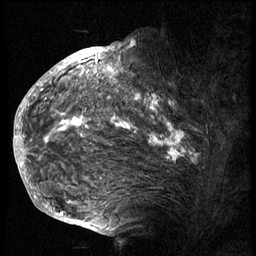
Breast MRI (dynamic contrast-enhanced), one sagittal slice. Slice 48 of 74 in the series (ordered by position). 3 images stored at this slice position (order not interpretable as contrast timing). 1.5 T. TE 4.2 ms, TR 8.9 ms. 2.5 mm slice thickness. 256 × 256 image matrix, field of view 200 × 200 mm. Female patient, age 57 years. Case-level facts recorded for this patient, not image findings: setting: breast cancer imaged before/during neoadjuvant chemotherapy; receptor status: HER2-positive.
Outlined on this slice (semi-automatic segmentation, software-assisted and operator-edited):
- analysis volume of interest (the breast-tissue region the enhancement analysis was run in; not a lesion): box from (x=40, y=62) to (x=240, y=175) px
- tumour enhancement mask (voxels above the 140 % enhancement threshold inside the analysis volume of interest): (x=41, y=62)–(x=191, y=161)